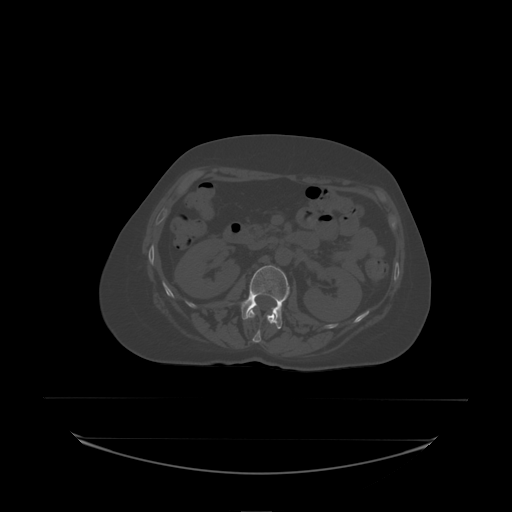
CT including the spine, one axial slice; position 76 of 242 along the scan axis; bone window (W 1800 / L 400 HU); 512 × 512 image matrix. Patient: female, 53 years. Case-level facts recorded for this patient, not image findings: primary cancer: lung.
Outlined on this slice (semi-automatically segmented with operator editing):
- L1 vertebra: box from (x=248, y=309) to (x=276, y=338) px
- L2 vertebra: (x=241, y=266)–(x=290, y=329)